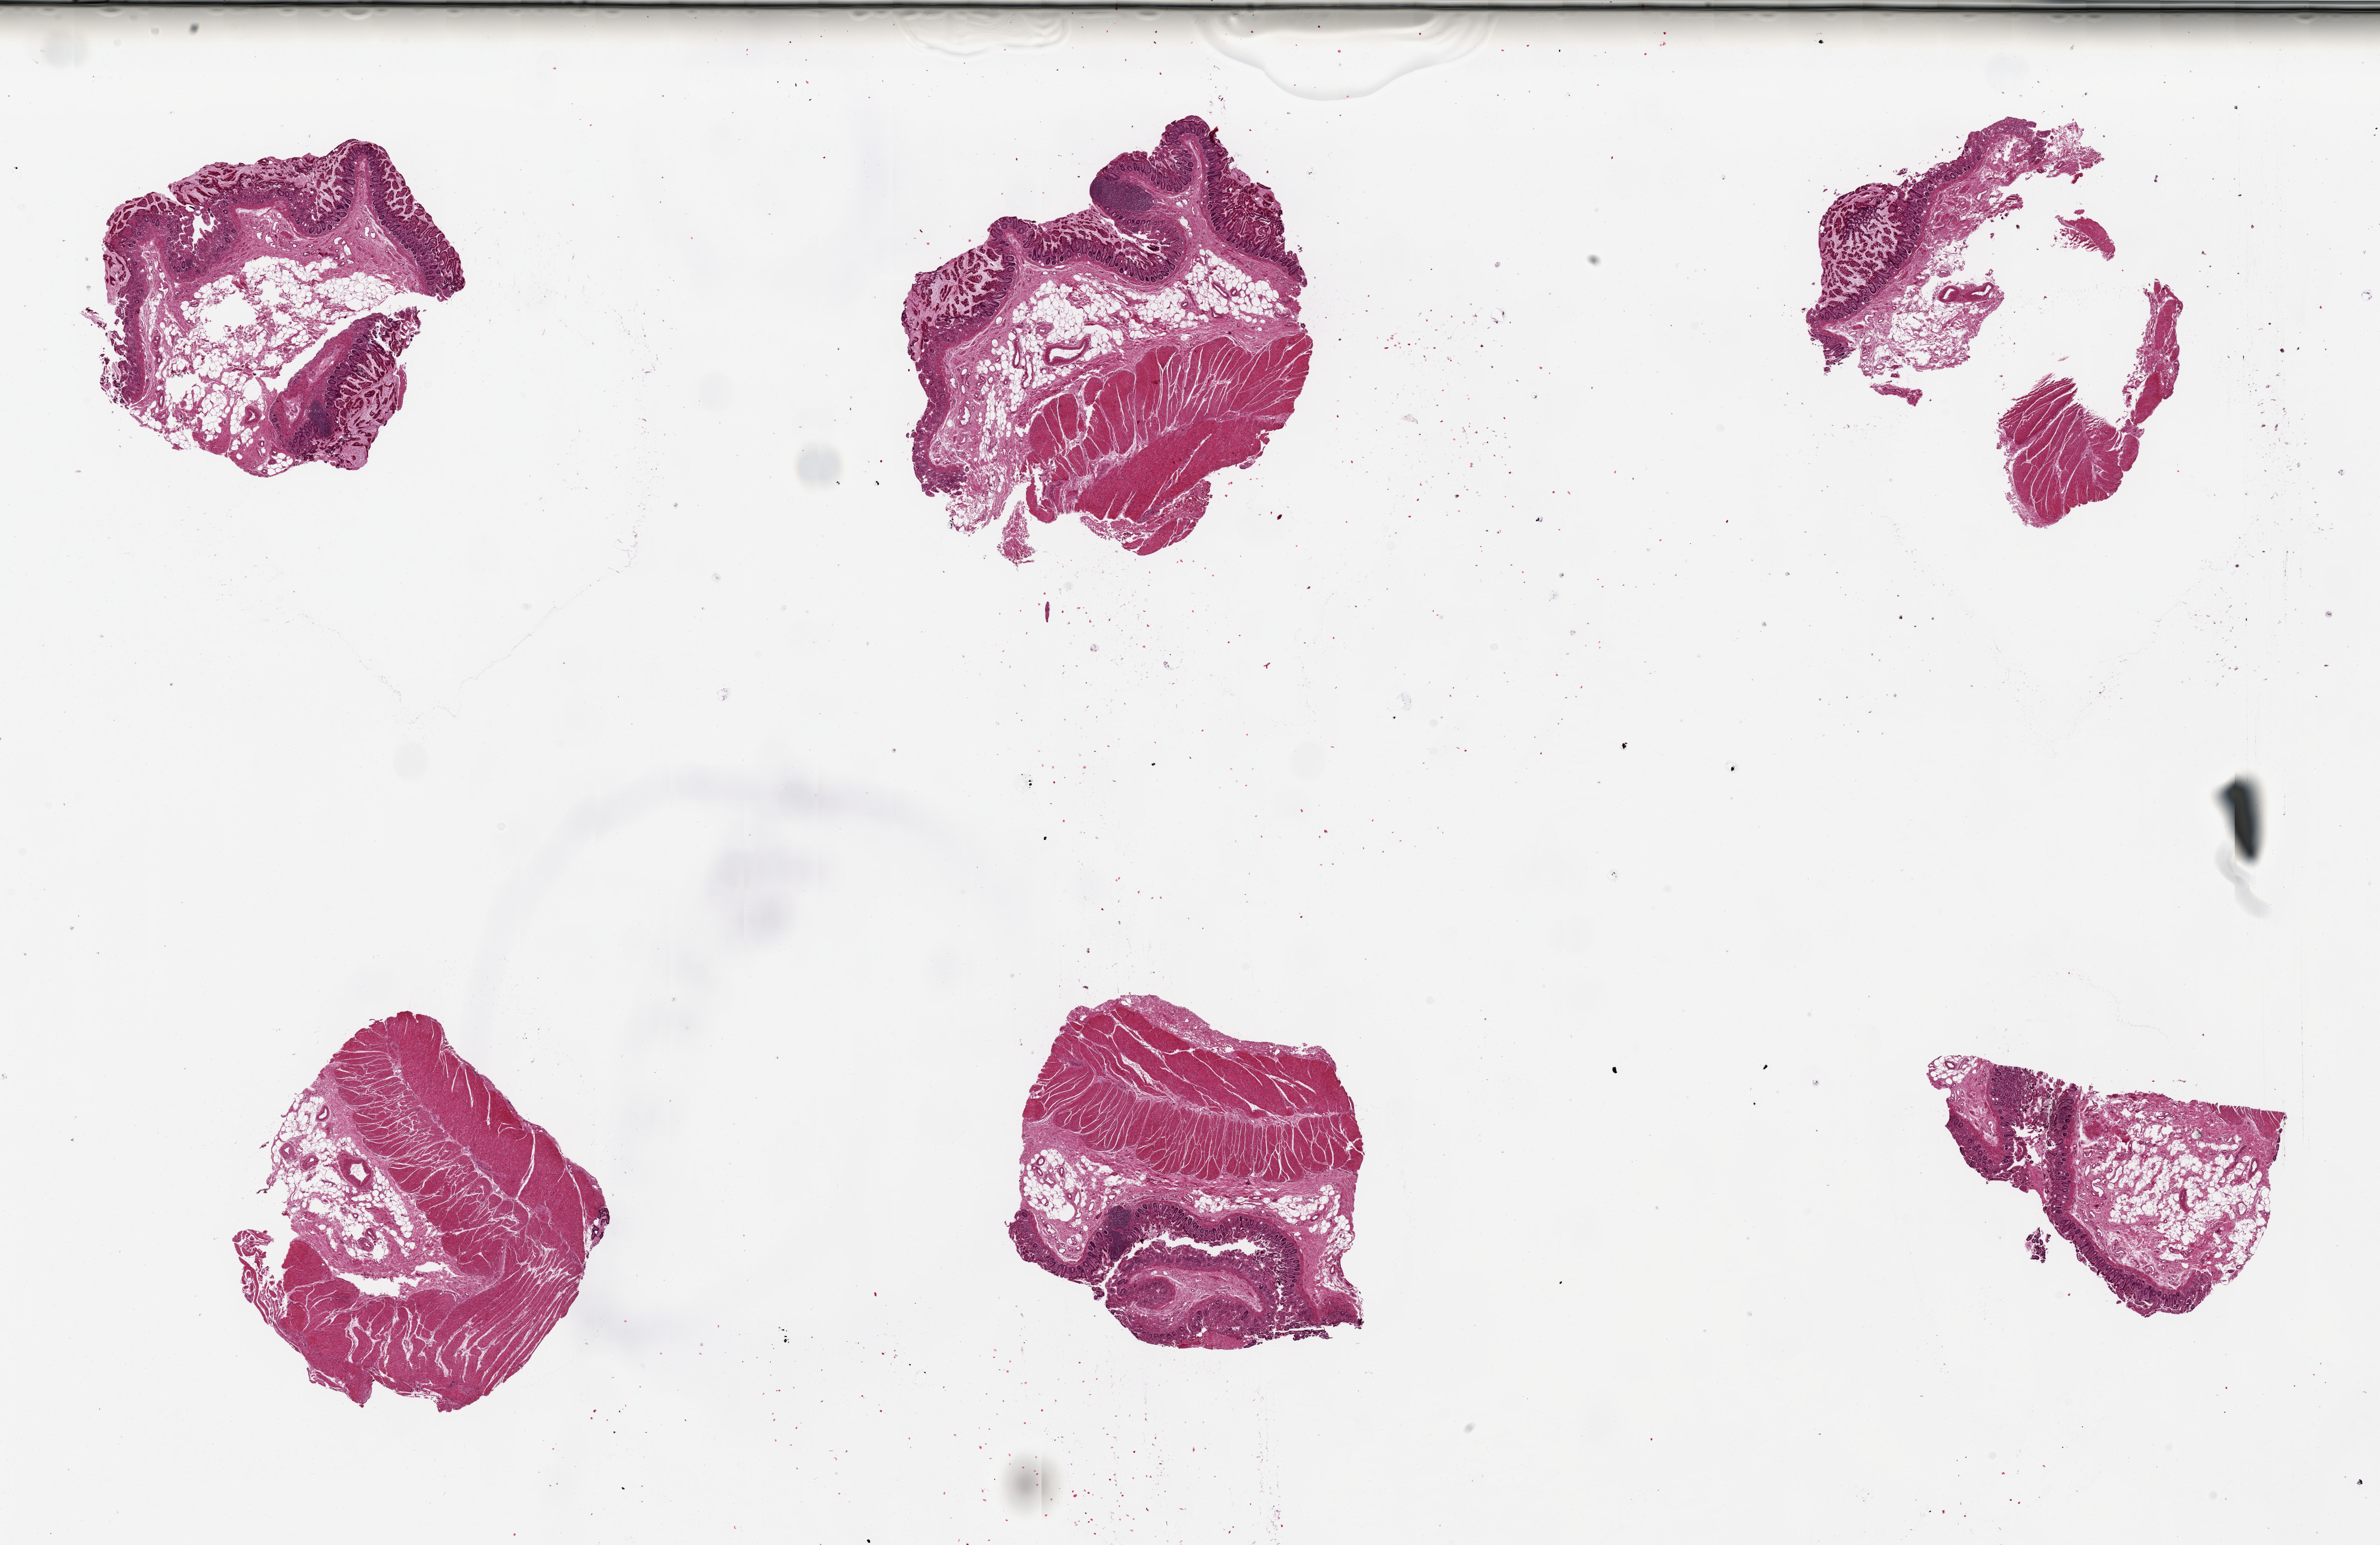
Digitized H&E-stained section, a low-resolution overview of the entire scanned area, about 31.5 x 20.4 mm; PAXgene-fixed paraffin-embedded (PFPE) section; target tissue: ileum; donor tissue sample. Donor sex: male.
Reviewer comment on this tissue sample: 6 pieces, up to 6x6mm; 3 small mucosal lymphoid nodules; well preserved mucosa.